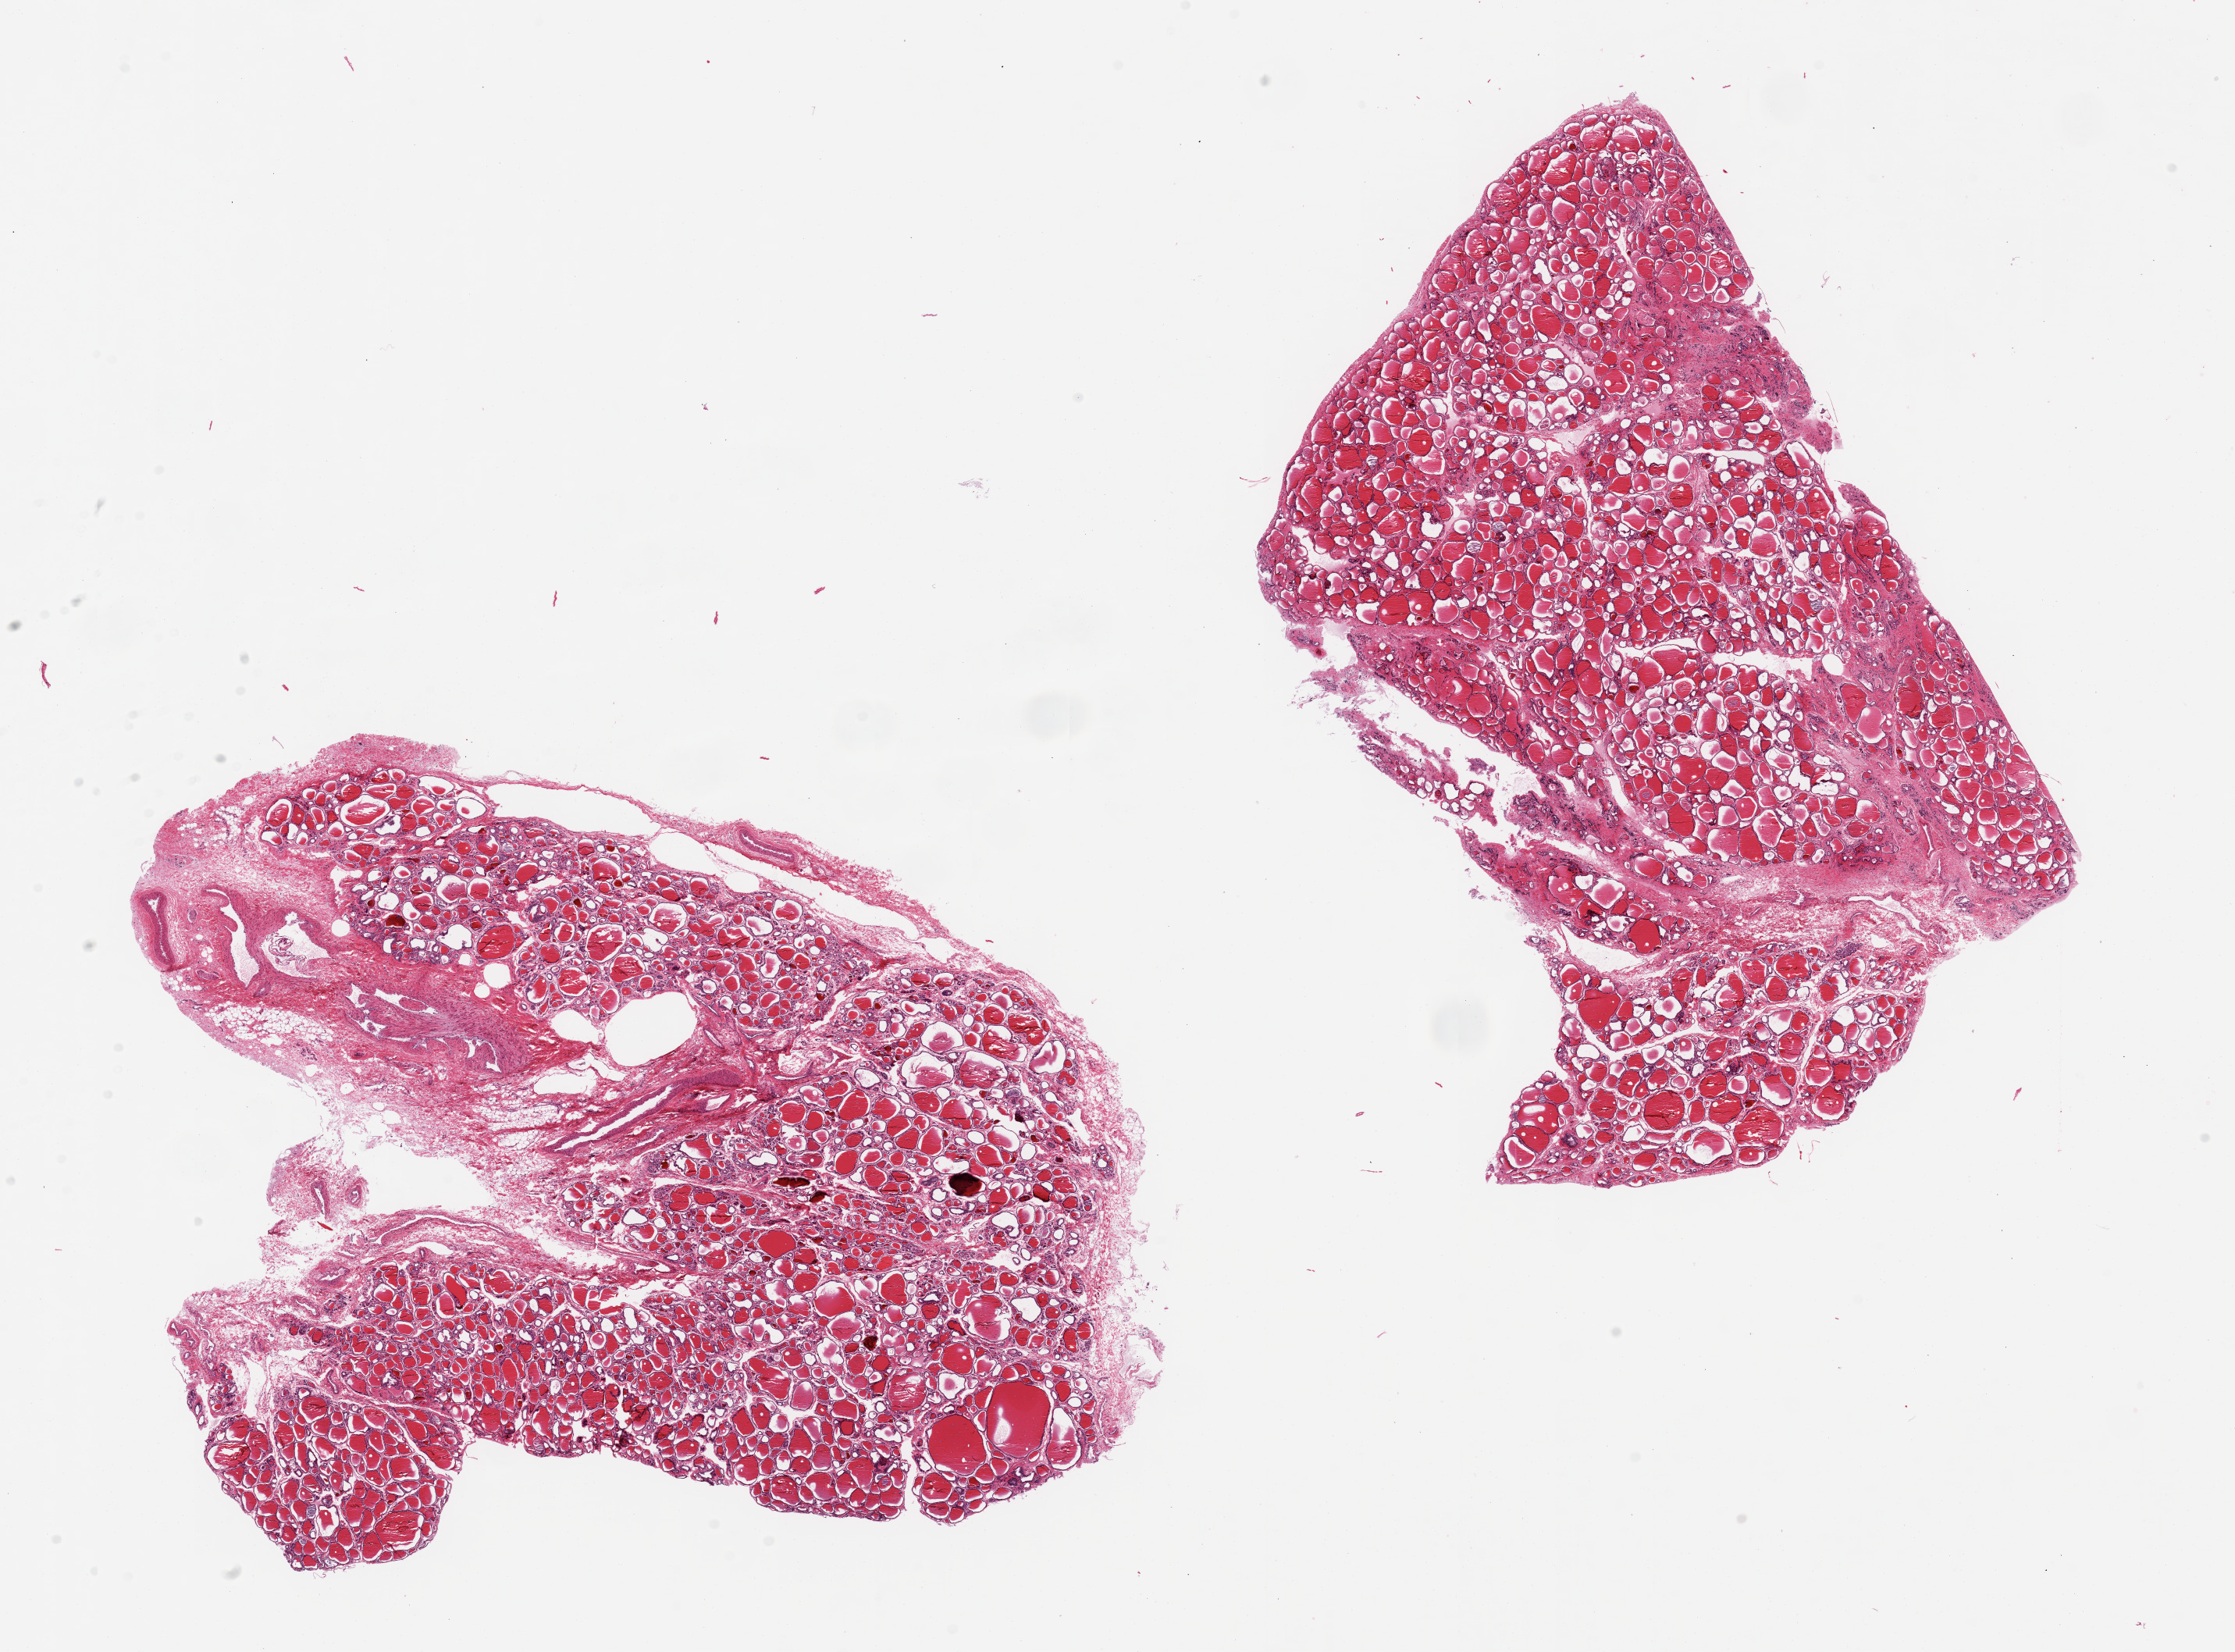
Whole-slide image, H&E stain — whole scanned area (about 22.6 x 16.7 mm) shown as a low-resolution overview; PAXgene-fixed paraffin-embedded (PFPE) section; section of thyroid (target tissue); tissue donor sample. Female donor.
Review note (as recorded): 2 pieces, adherent fat/fibrous tissue up to ~1.5mm.